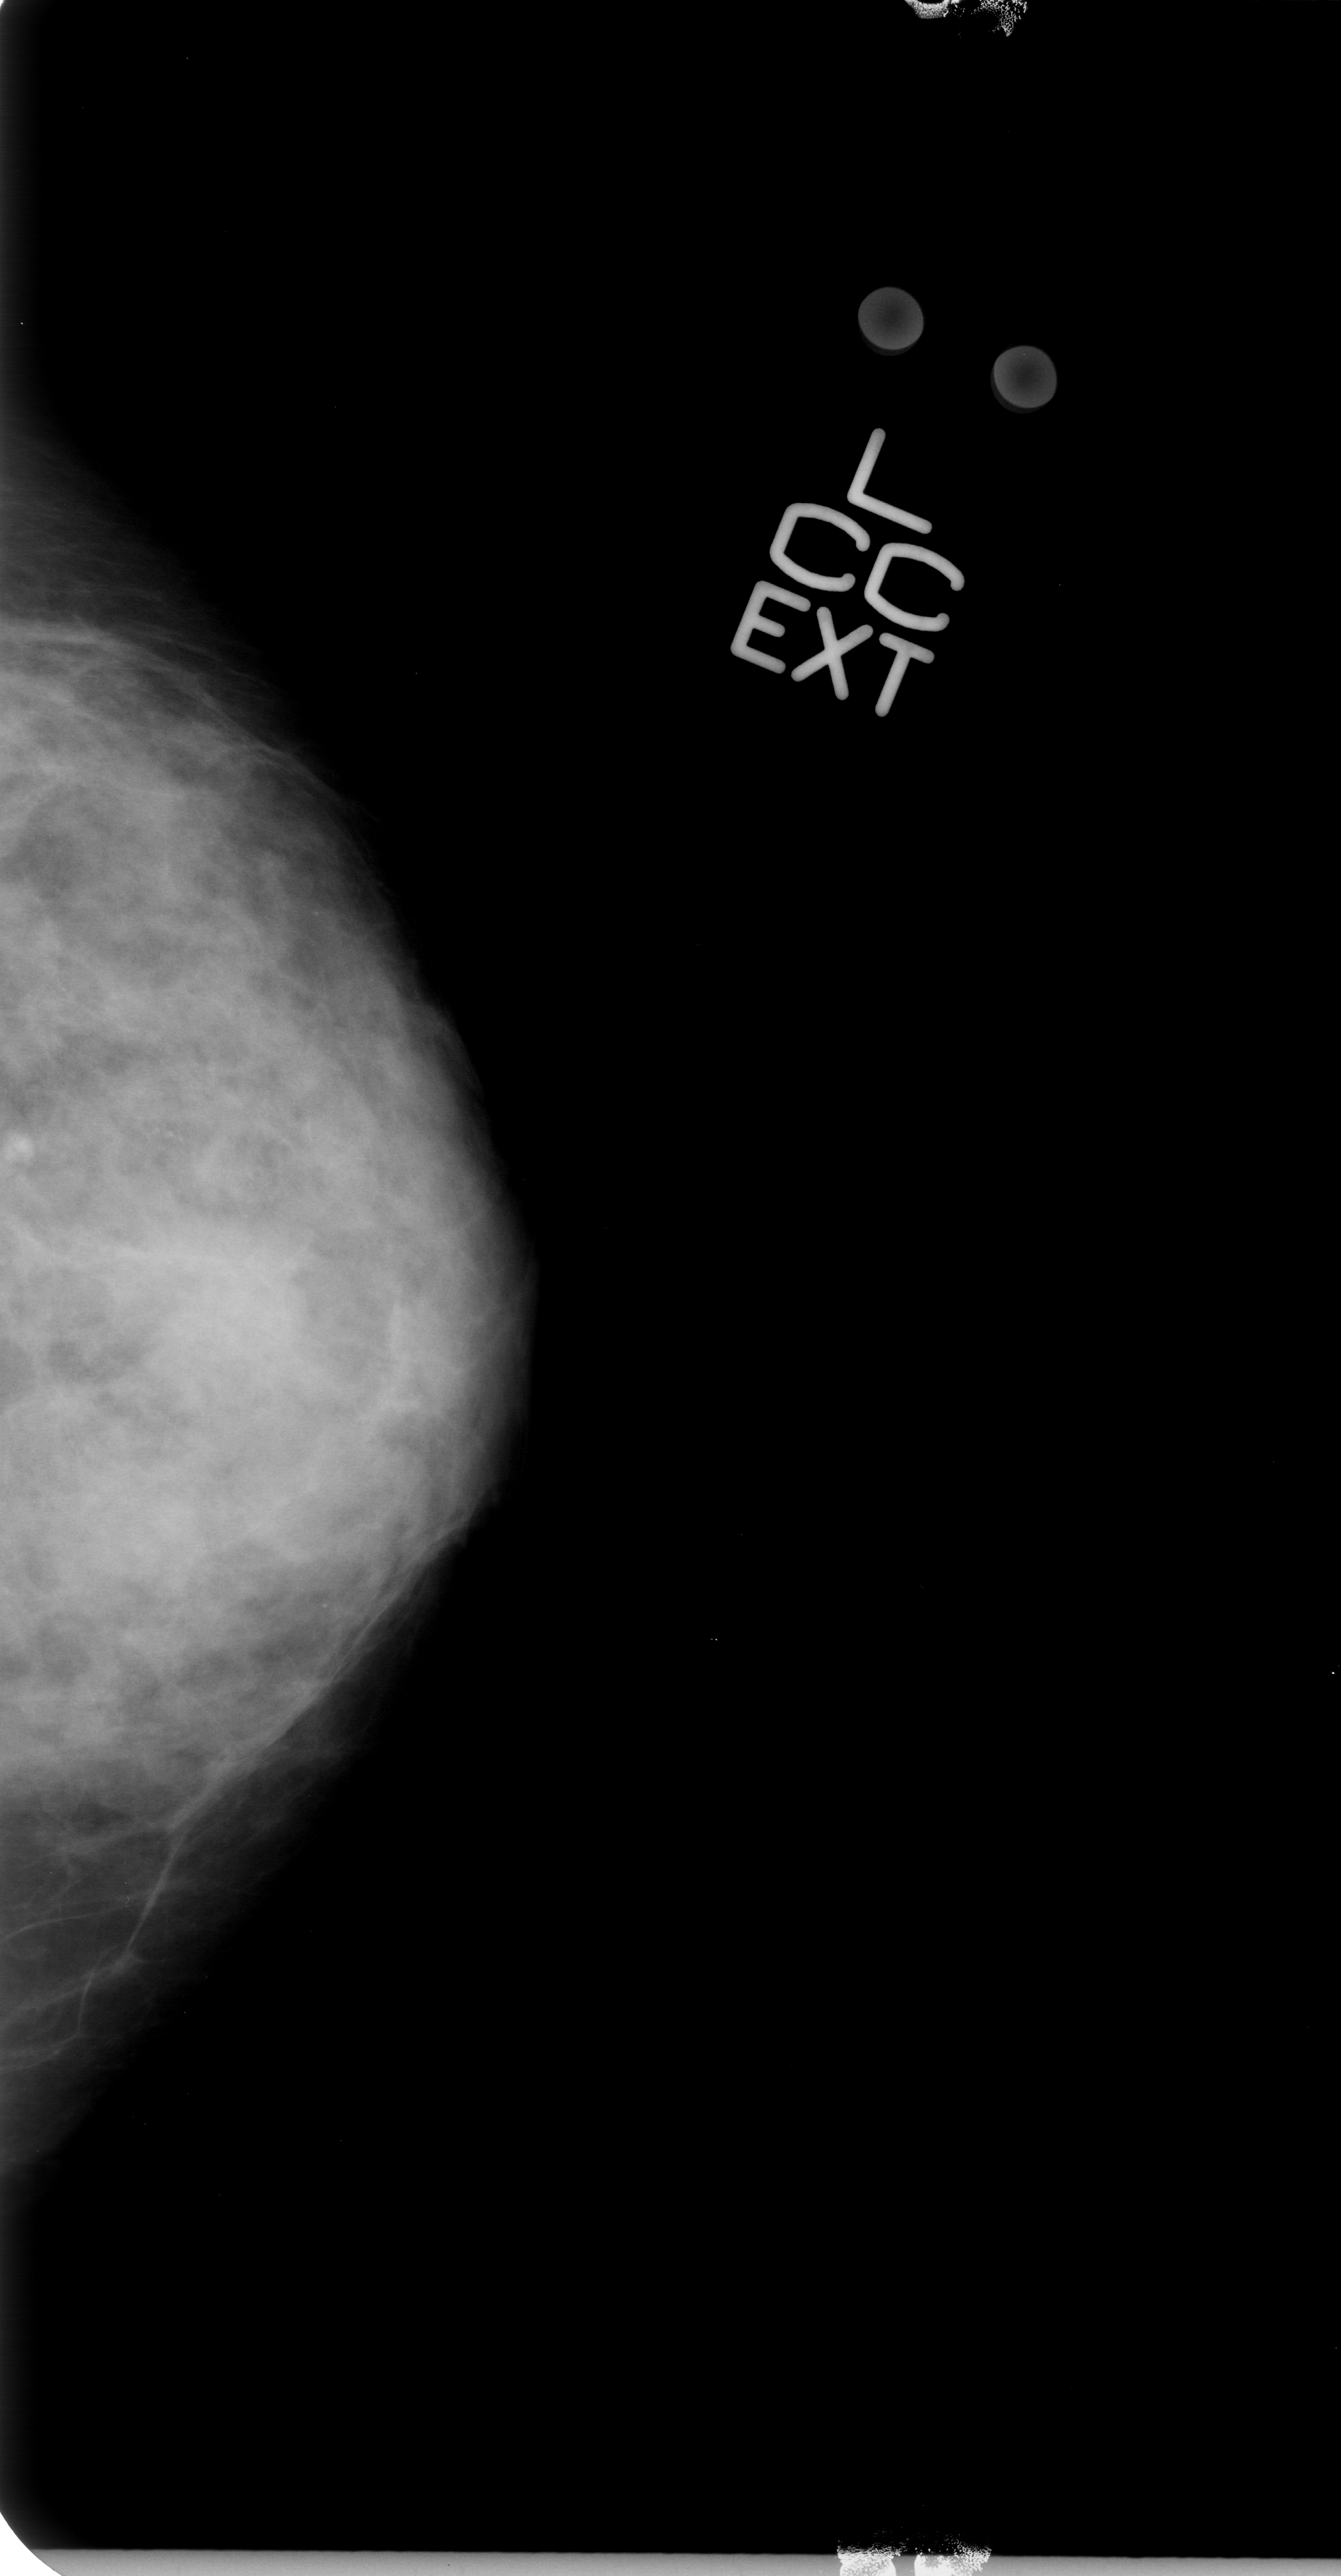
Digitized screen-film mammogram; left breast; CC view; BI-RADS breast density category 4 (scale 1–4).
Finding: mass, shape lobulated / architectural distortion, margins obscured / ill defined; BI-RADS assessment category 4; pathology result (as recorded, not read from the image): malignant.